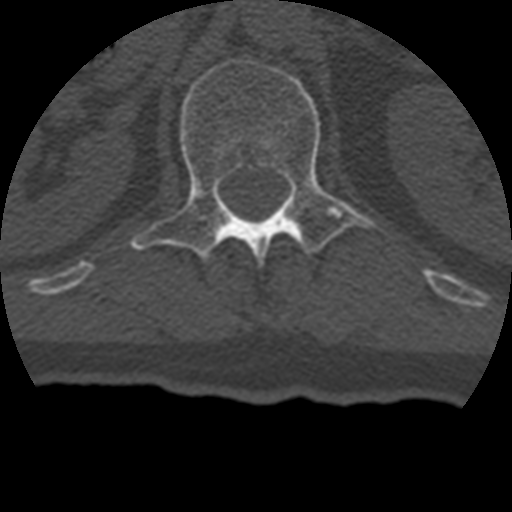
CT including the spine, one axial slice; slice 147 of 399 in the series (ordered by position); reconstruction kernel STANDARD; bone window (W 1800 / L 400 HU); 512 × 512 image matrix, field of view 160 × 160 mm. Patient age 69 years. Case-level facts recorded for this patient, not image findings: primary cancer: prostate.
Structures marked on this image (semi-automatic segmentation, software-assisted and operator-edited):
- L1 vertebra: bounding box <130,55,376,263> (left, top, right, bottom; pixels)